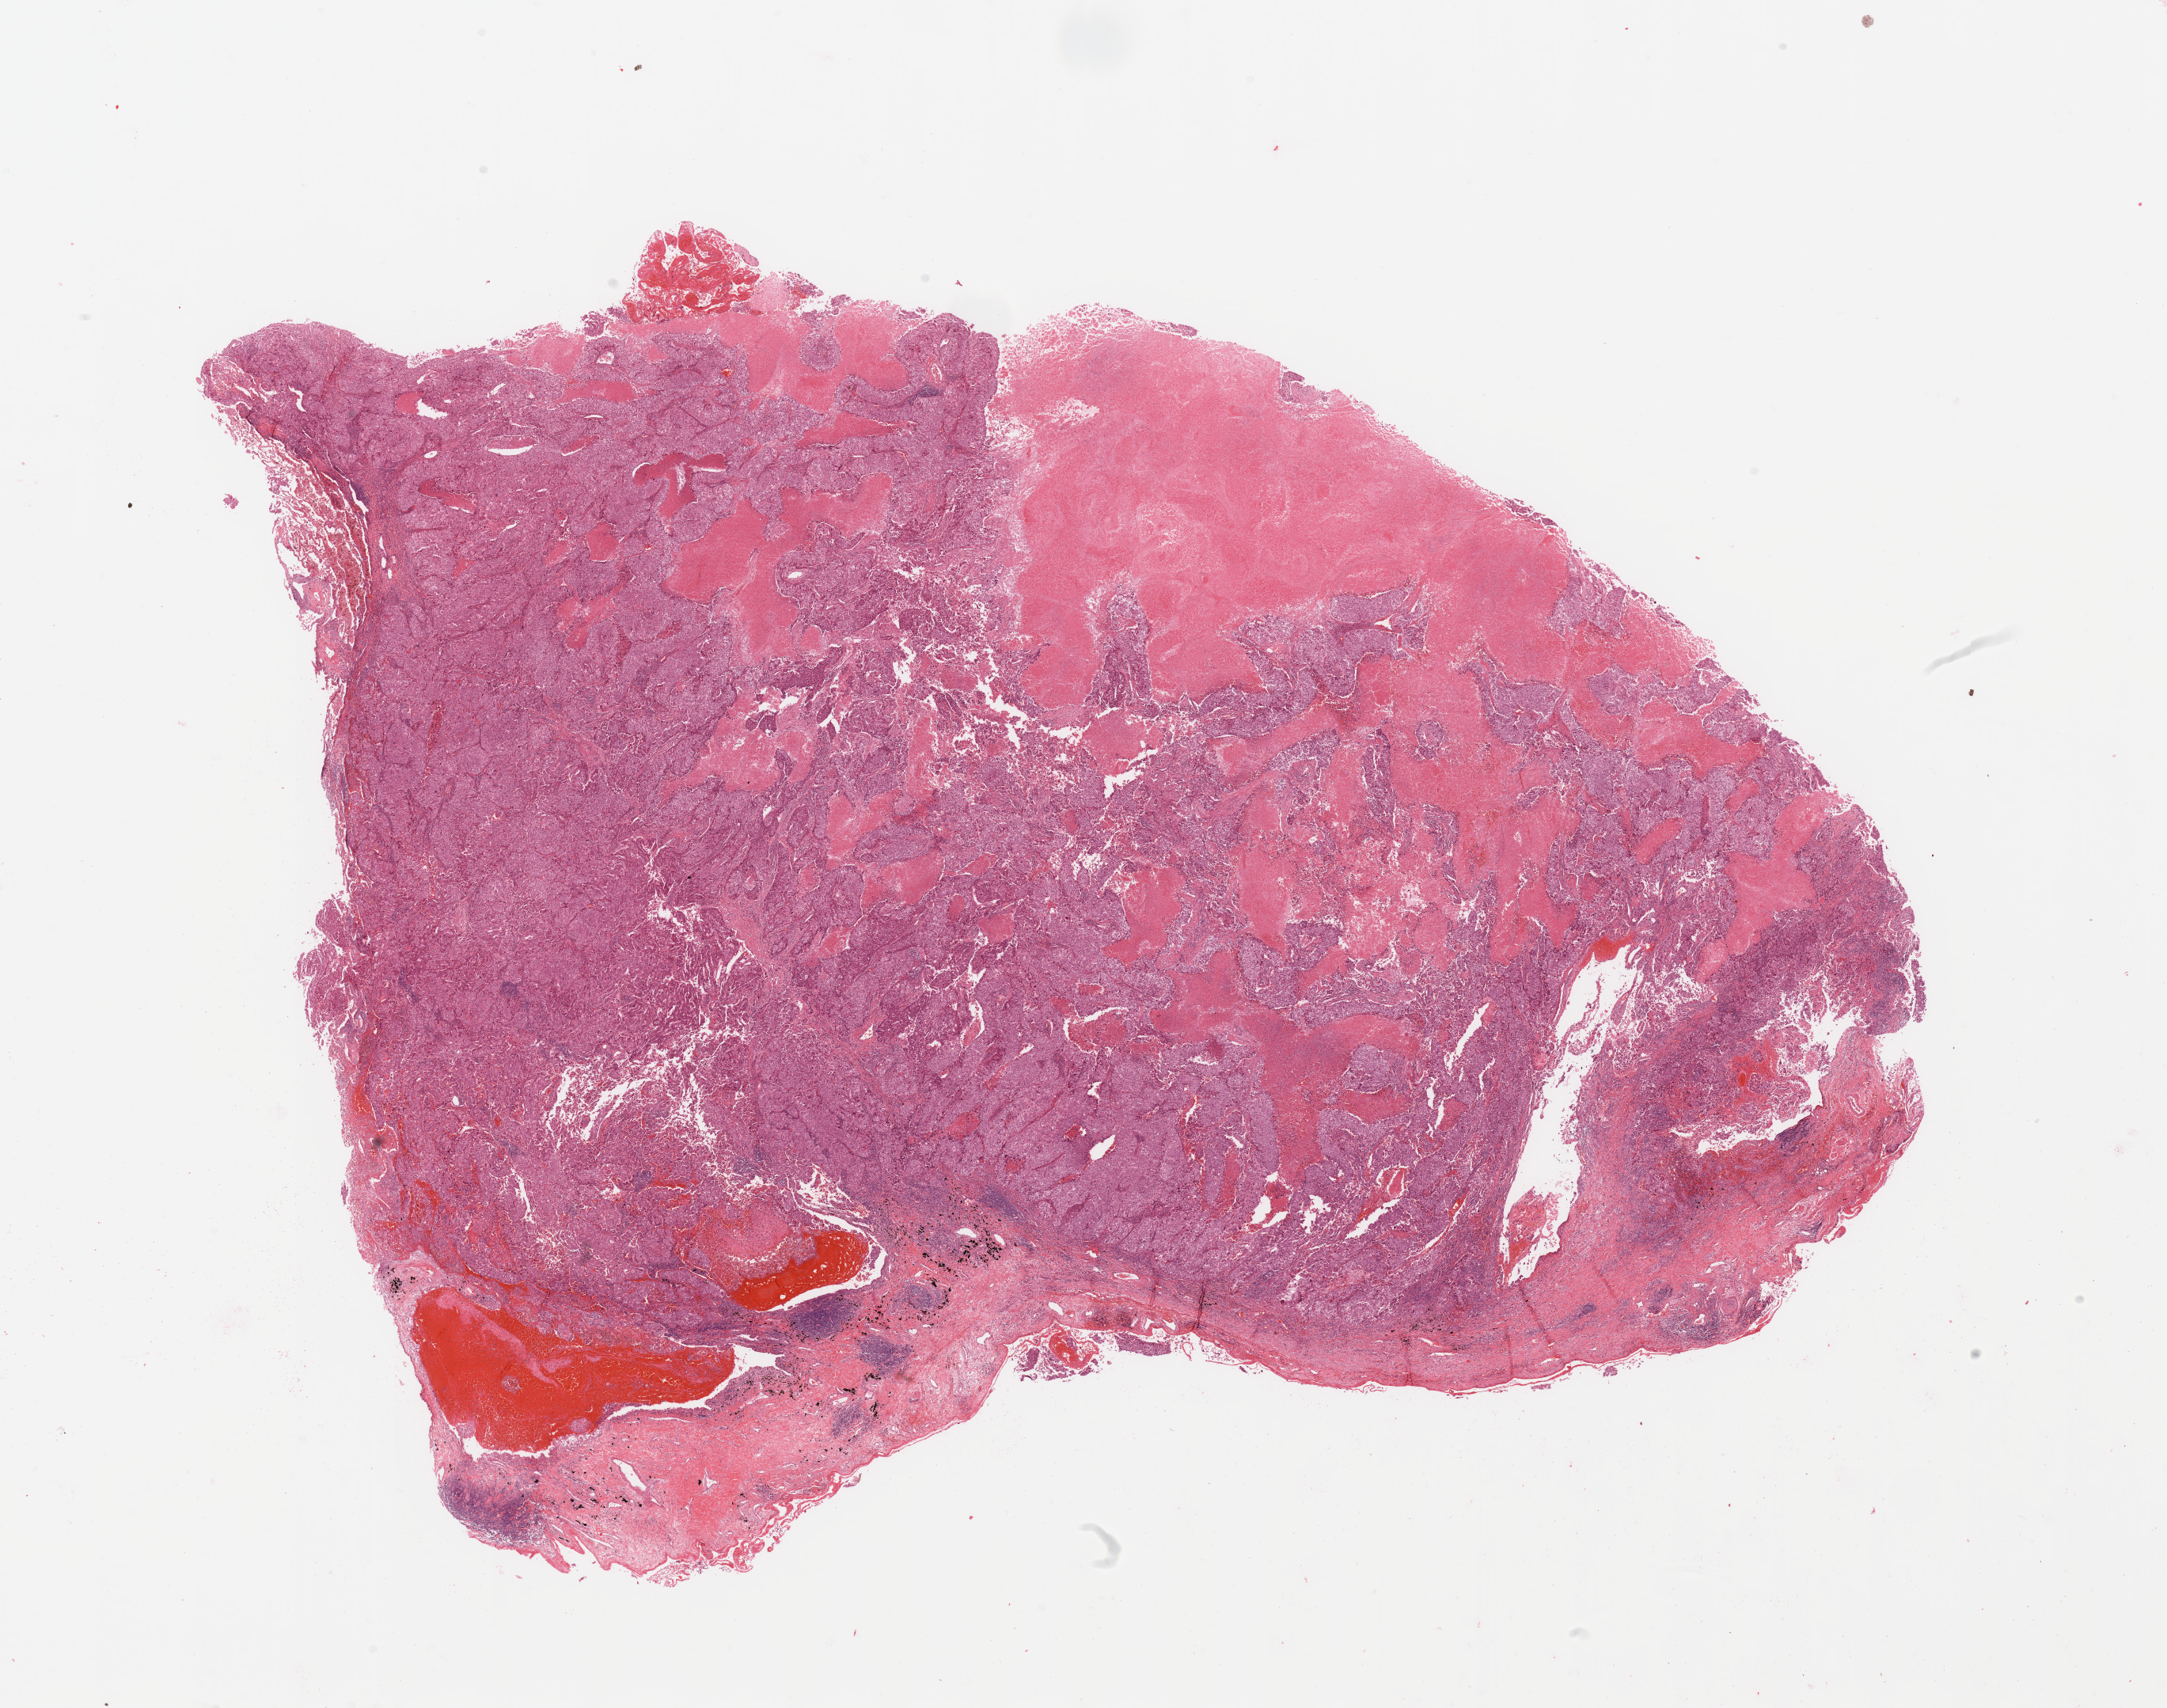
Whole-slide histology image, H&E-stained — shown as a low-resolution overview of the whole scanned area (about 21.7 x 17.1 mm, from a 20x scan). Tumour tissue sample, lung. 59-year-old male patient.
Histologic diagnosis: Adenocarcinoma, NOS.